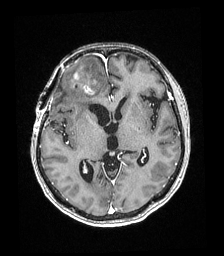
Brain MRI from a brain-tumour surgery series, one axial slice. T1-weighted post-contrast. 224 × 256 image matrix, field of view 219 × 250 mm. Case-level facts recorded for this patient, not image findings: histopathology: Astrocytoma; WHO grade: 4; IDH mutation: yes; tumour location: Right superficial frontal.
Annotated regions visible in this slice (outlined manually by an expert reader):
- tumour: bounding box <74,74,92,94> (left, top, right, bottom; pixels)